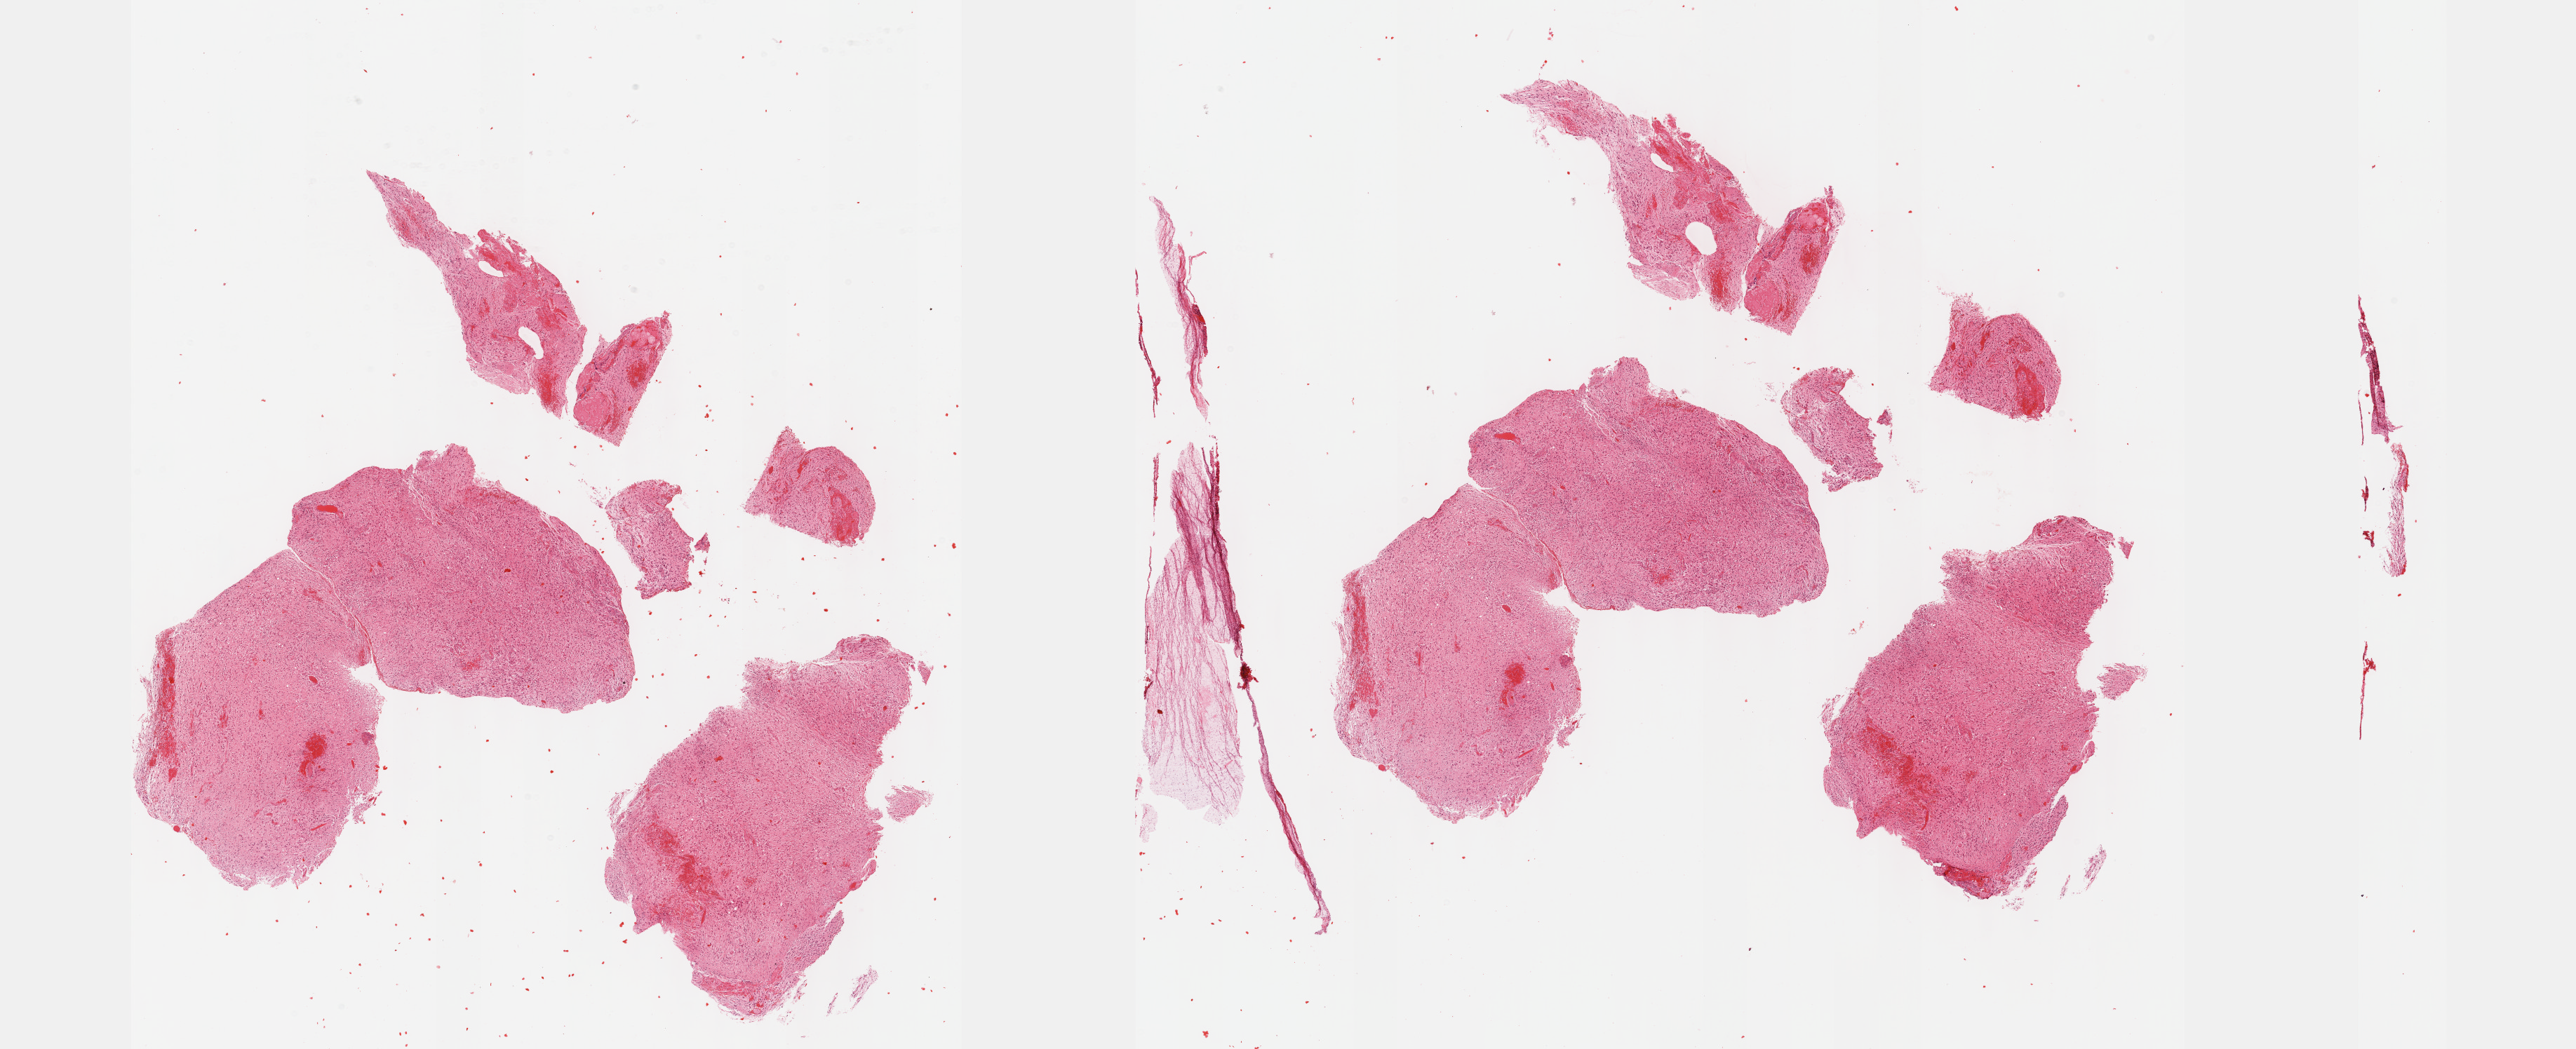
H&E whole-slide image — whole scanned area (about 29.7 x 12.1 mm, slide scanned at 40x) shown as a low-resolution overview, formalin-fixed paraffin-embedded (FFPE) diagnostic section, brain, primary tumour sample. Male, age 70 years at initial diagnosis. Histologic grade: G3 (poorly differentiated).
• histologic diagnosis: Astrocytoma, anaplastic